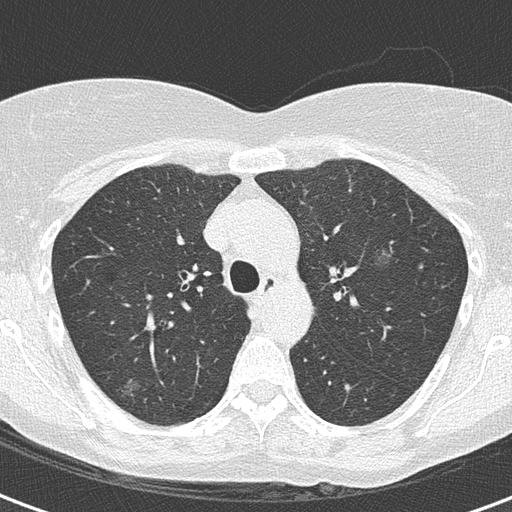
Axial slice from a low-dose chest CT screening exam, second screening round (one year after baseline), lung window (W 1500 / L -600 HU), 2 mm slice thickness, slice 49 of 172 in the series, 512 × 512 image matrix. Female participant, aged 56 years at enrolment. Current smoker at enrolment.
Expert-annotated lung lesion, bounding box [x1, y1, x2, y2] px = [87, 369, 155, 423]. Screening reader's record for this exam (one nodule recorded; not confirmed to be the boxed lesion): non-calcified nodule or mass ≥4 mm, right upper lobe, 18 × 18 mm, mixed attenuation, pre-existing on the prior screen: yes.